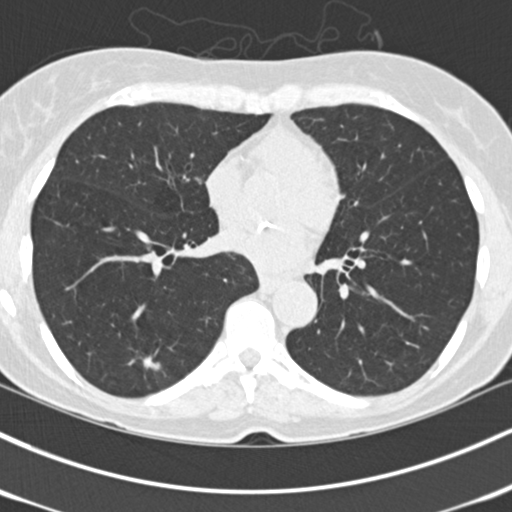
Low-dose screening chest CT, one axial slice; position 62 of 150 along the scan axis; 120 kVp; lung window (W 1500 / L -600 HU); 2 mm slice thickness; 512 × 512 image matrix, field of view 318 × 318 mm.
Outlined on this slice (manually delineated by an expert):
- lesion 1 (tumor): bounding box <144,357,160,370> (left, top, right, bottom; pixels)